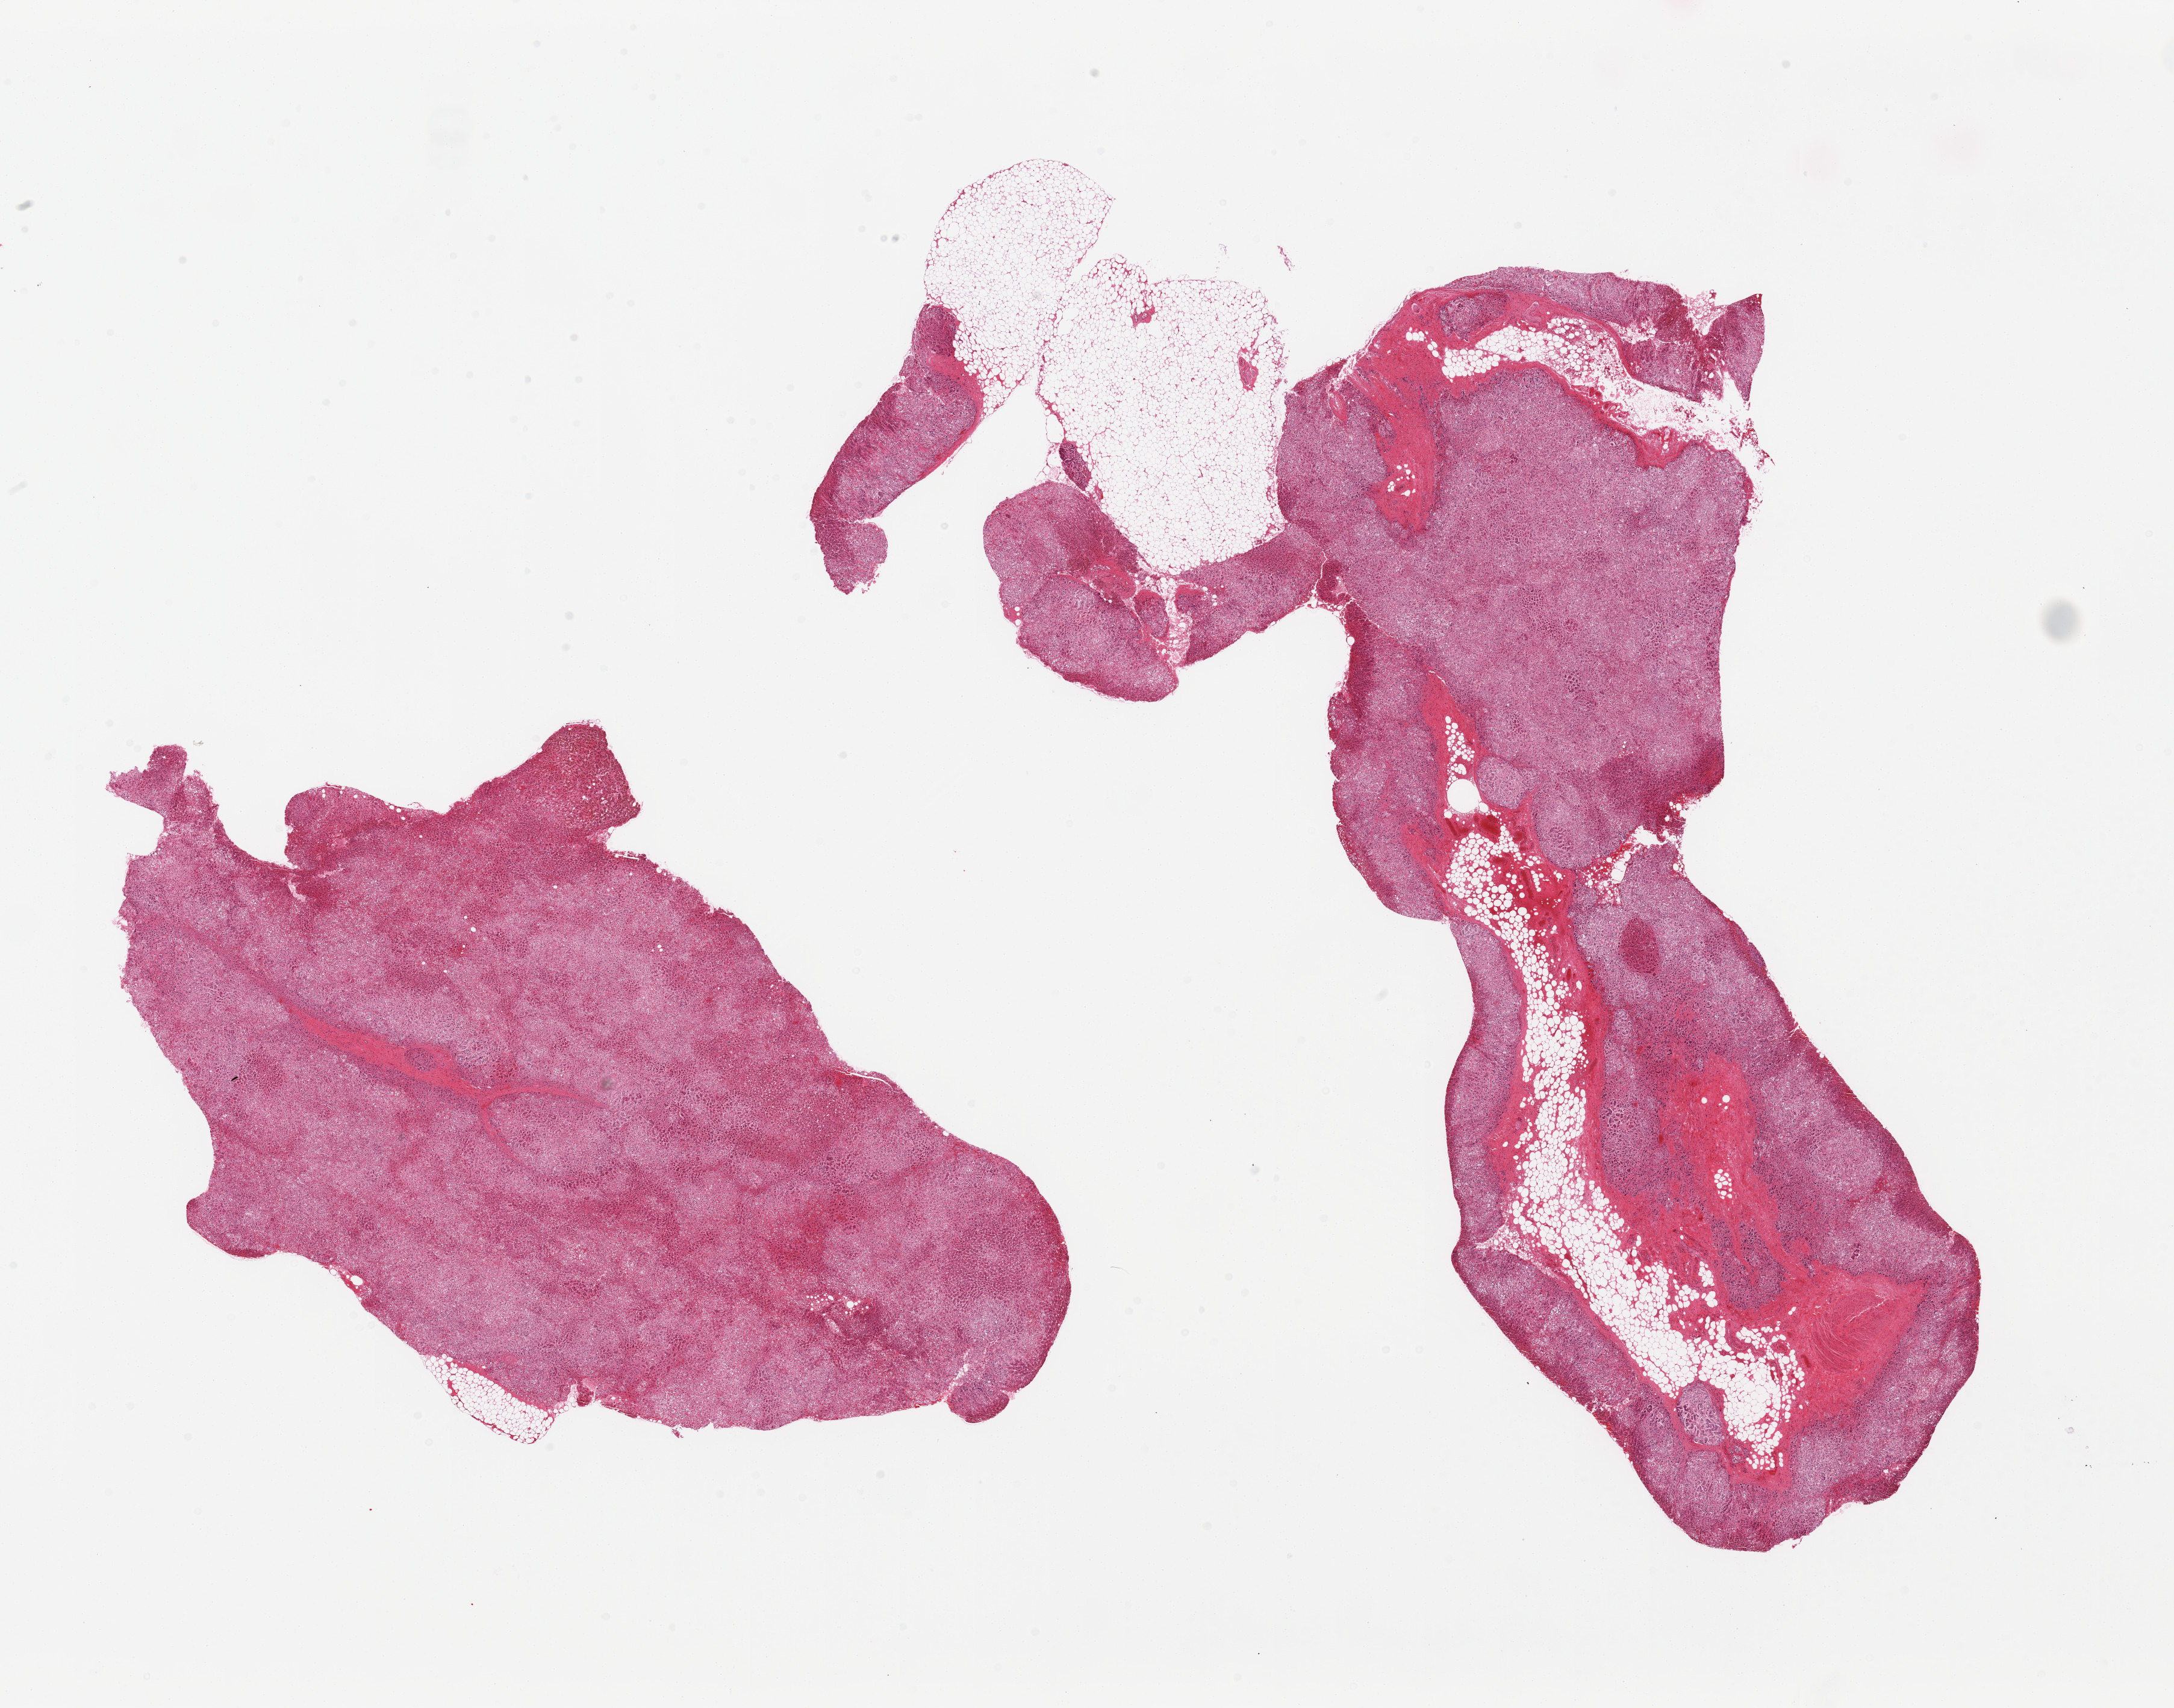
Whole-slide image, hematoxylin and eosin (H&E) stain, shown as a low-resolution overview of the whole scanned area (about 28.5 x 22.4 mm), PAXgene-fixed, paraffin-embedded tissue, target tissue: adrenal gland, donor tissue sample. Male donor.
* review note (as recorded): 2 pieces, all cortex, ~10% interstitial fat, moderatly-markedly autolzyed